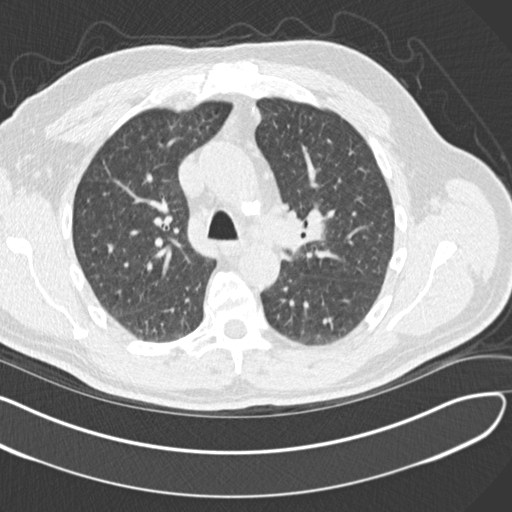
Chest CT (low-dose screening protocol), one axial image. Second screening round (one year after baseline). Lung window (W 1500 / L -600 HU). 2 mm slice thickness. 512 × 512 image matrix. Male participant, aged 65 years at enrolment. Former smoker at enrolment.
- Expert reader's lesion annotation, bounding box <288,196,349,260> (left, top, right, bottom; pixels).
- The screening reader recorded 4 non-calcified nodules or masses ≥4 mm on this exam (left upper lobe, left upper lobe, left lower lobe, right middle lobe); which of them this box marks is not recorded.
- Participant outcome: lung cancer diagnosed 577 days after this screen (after the third annual screen) — acinar cell carcinoma, left upper lobe, stage IA (AJCC 6th edition), 25 mm at pathology.